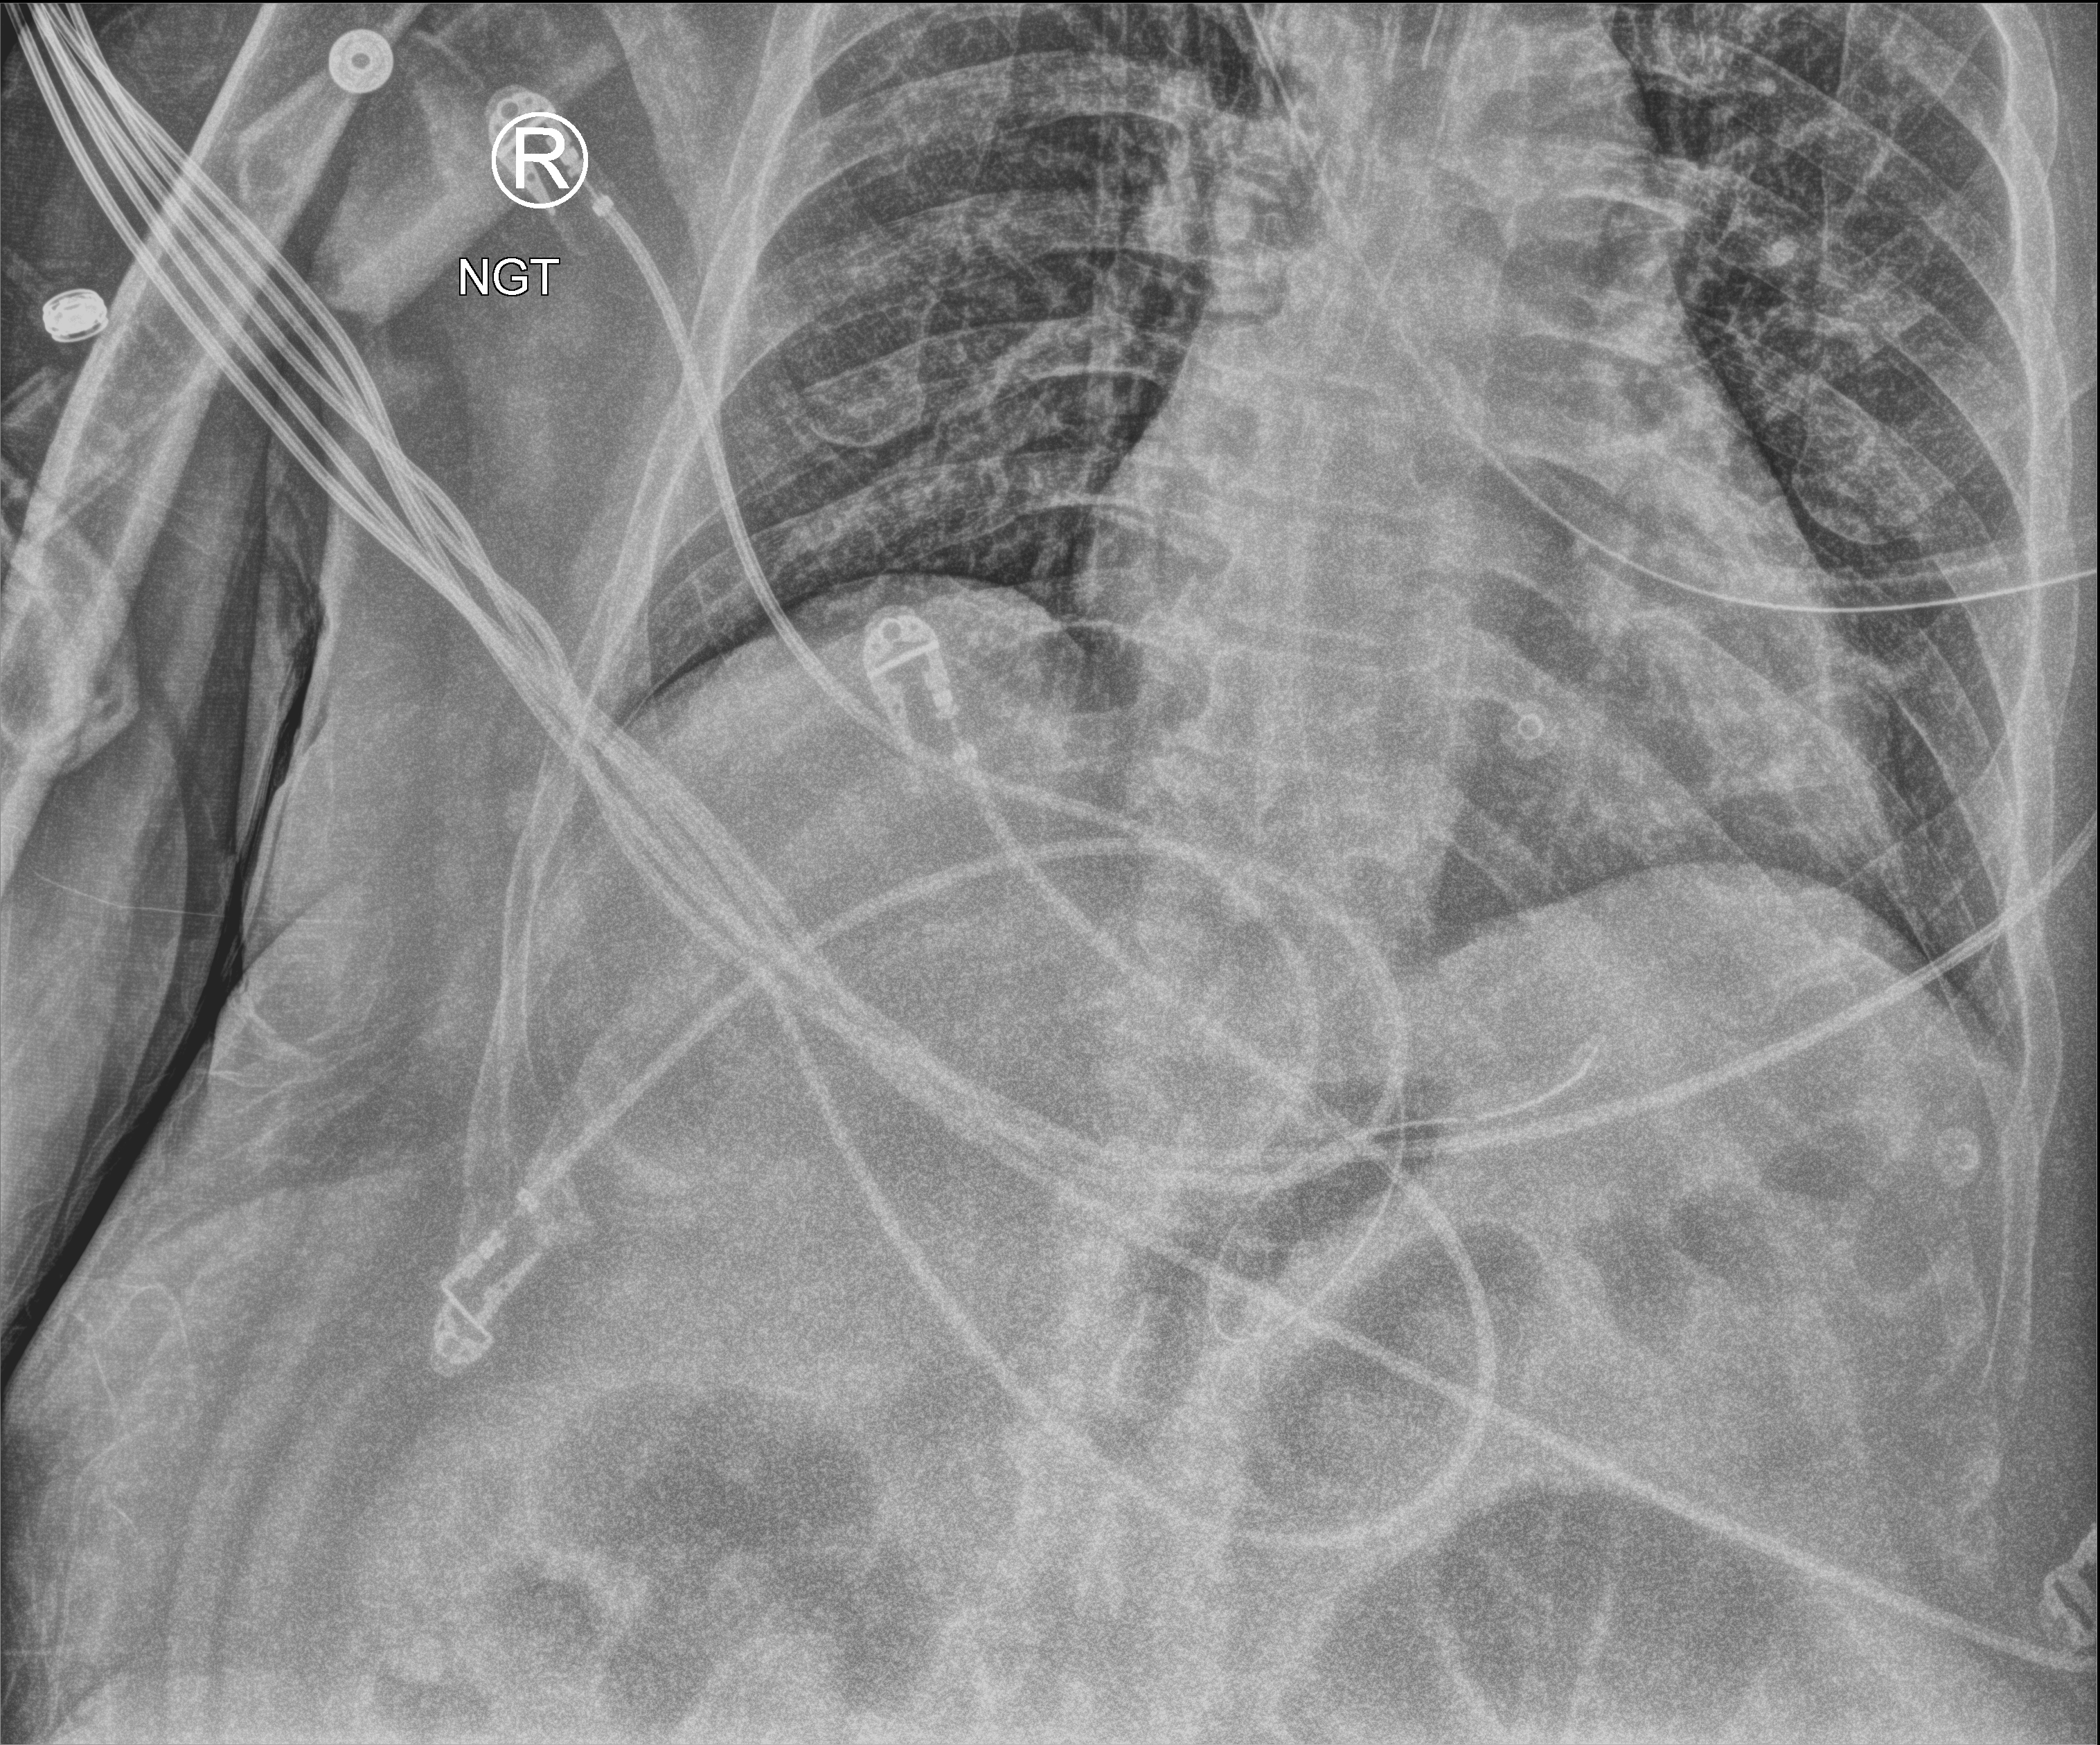
Bedside chest radiograph (computed radiography); anteroposterior (AP) projection. Adult patient hospitalised with COVID-19, age 18–59 years.
Hospital-stay facts (about this admission, not read from this image; timing relative to this image not recorded):
- mechanically ventilated during this hospital stay: yes
- other chronic lung disease (admission record): no
- length of hospital stay: 37 days